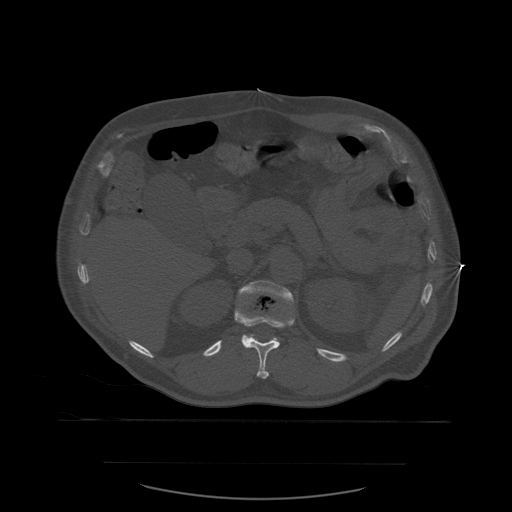
CT including the spine, one axial slice; position 264 of 590 along the scan axis; bone window (W 1800 / L 400 HU); 1.25 mm slice thickness; 512 × 512 image matrix. Patient age 71 years. From the clinical record (not read from this slice): primary cancer: lung; vertebrae with lytic lesions (as recorded): T1, T2, L5, S1.
Structures marked on this image (semi-automatically segmented with operator editing):
- L1 vertebra: bounding box <239,281,295,340> (left, top, right, bottom; pixels)
- T12 vertebra: <235,307,295,379>